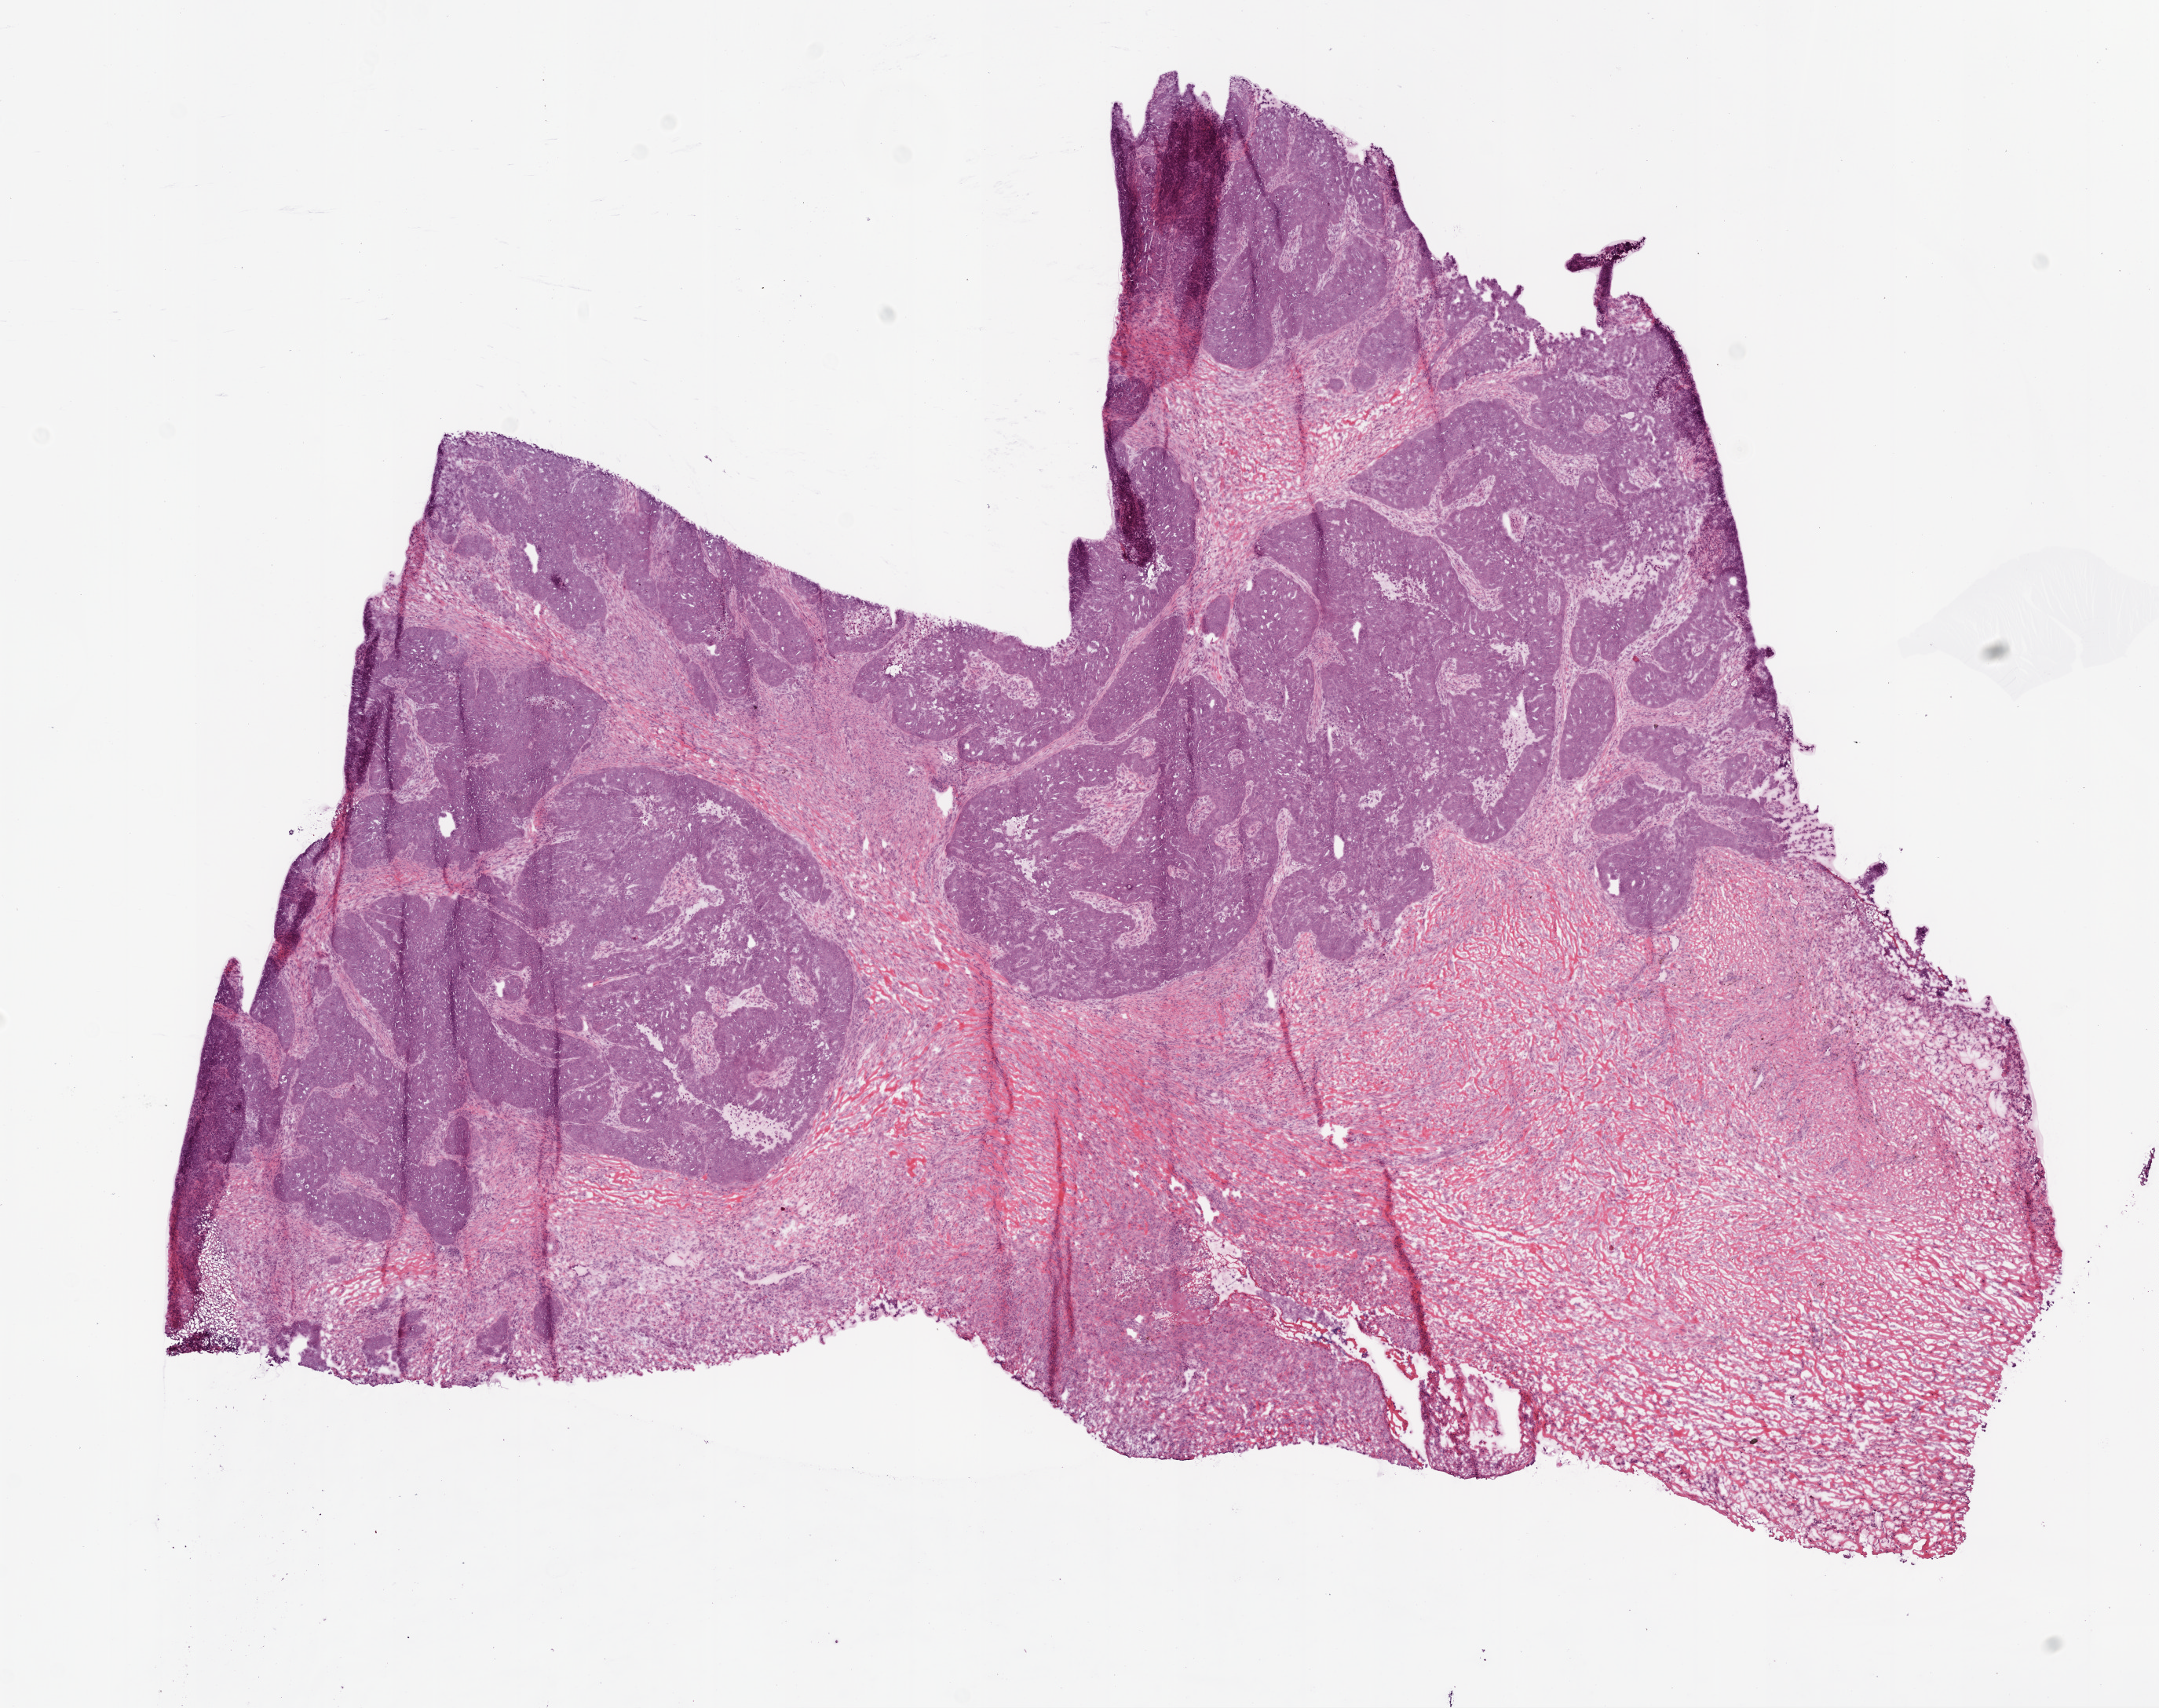
H&E-stained whole-slide image, low-resolution overview of the scanned area, about 11.0 x 8.7 mm (from a 20x scan); frozen section from the bottom of the tissue portion; ovary, primary tumour sample. Patient: female, age at initial diagnosis 48 years. Histologic grade: G3 (poorly differentiated). Slide review estimates, as recorded: tumour cells 80%, tumour nuclei 80%, normal cells 0%, stromal cells 20%, necrosis 0%.
Histologic diagnosis: Serous cystadenocarcinoma, NOS. FIGO stage: IIIC.